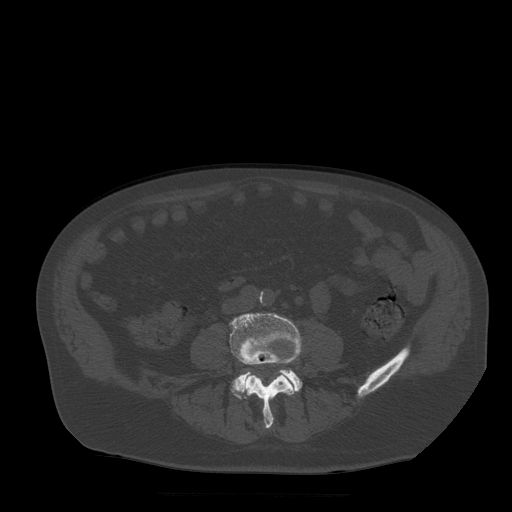
CT including the spine, one axial slice. Slice 107 of 522 in the series (ordered by position). Bone window (W 1800 / L 400 HU). 512 × 512 image matrix, field of view 420 × 420 mm. Patient age 72 years. From the clinical record (not read from this slice): primary cancer: prostate.
Outlined on this slice (semi-automatically segmented with operator editing):
- L4 vertebra: bounding box <230,314,302,429> (left, top, right, bottom; pixels)
- L5 vertebra: <232,370,302,400>